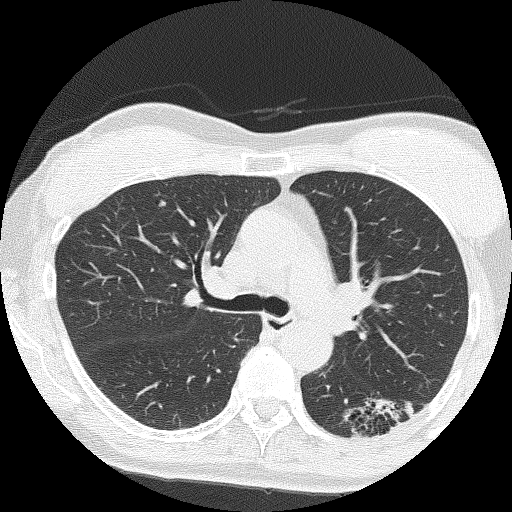
Axial slice from a low-dose chest CT screening exam. Second annual screen. Lung window (W 1500 / L -600 HU). Lung (sharp) reconstruction kernel (FC51). Slice 58 of 159 in the series. Female, age 64 years at enrolment.
Expert reader's lesion annotation, bounding box <355,385,422,439> (left, top, right, bottom; pixels). The screening reader recorded 3 non-calcified nodules or masses ≥4 mm on this exam (right upper lobe, right upper lobe, right middle lobe); which of them this box marks is not recorded. Lung cancer was diagnosed 576 days after this screen (after the third annual screen): adenocarcinoma, NOS, left lower lobe, moderately differentiated (G2), stage IA (AJCC 6th edition), 17 mm at pathology.